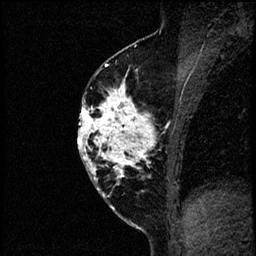
Breast MRI (dynamic contrast-enhanced), one sagittal slice. Slice 35 of 60 in the series (ordered by position). Dynamic contrast-enhanced study with each time point stored as its own series, time point 2 of 4 at this slice position (early post-contrast, ordered by acquisition time). 1.5 T. TE 4.2 ms, TR 17.6 ms. 256 × 256 image matrix, field of view 200 × 200 mm. Patient: female, 40 years. From the clinical record (not read from this slice): setting: breast cancer imaged before/during neoadjuvant chemotherapy; receptor status: HER2-positive.
Annotated regions visible in this slice (semi-automatic segmentation, software-assisted and operator-edited):
- analysis volume of interest (the breast-tissue region the enhancement analysis was run in; not a lesion): bounding box (x1, y1, x2, y2) in pixels: (79, 56, 197, 205)
- tumour enhancement mask (voxels above the 100 % enhancement threshold inside the analysis volume of interest): (79, 64, 190, 196)